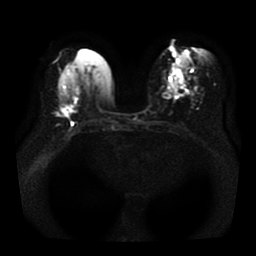
Breast MRI, one axial slice. Slice 17 of 41 in the series (ordered by position). Diffusion-weighted series; image 2 of 4 stored at this slice position (different b-values; order by instance number). 1.5 T. 5 mm slice thickness. 256 × 256 image matrix. Female patient.
Structures marked on this image (outlined manually by an expert reader):
- tumour on diffusion-weighted imaging: bounding box (x1, y1, x2, y2) in pixels: (57, 107, 76, 117)